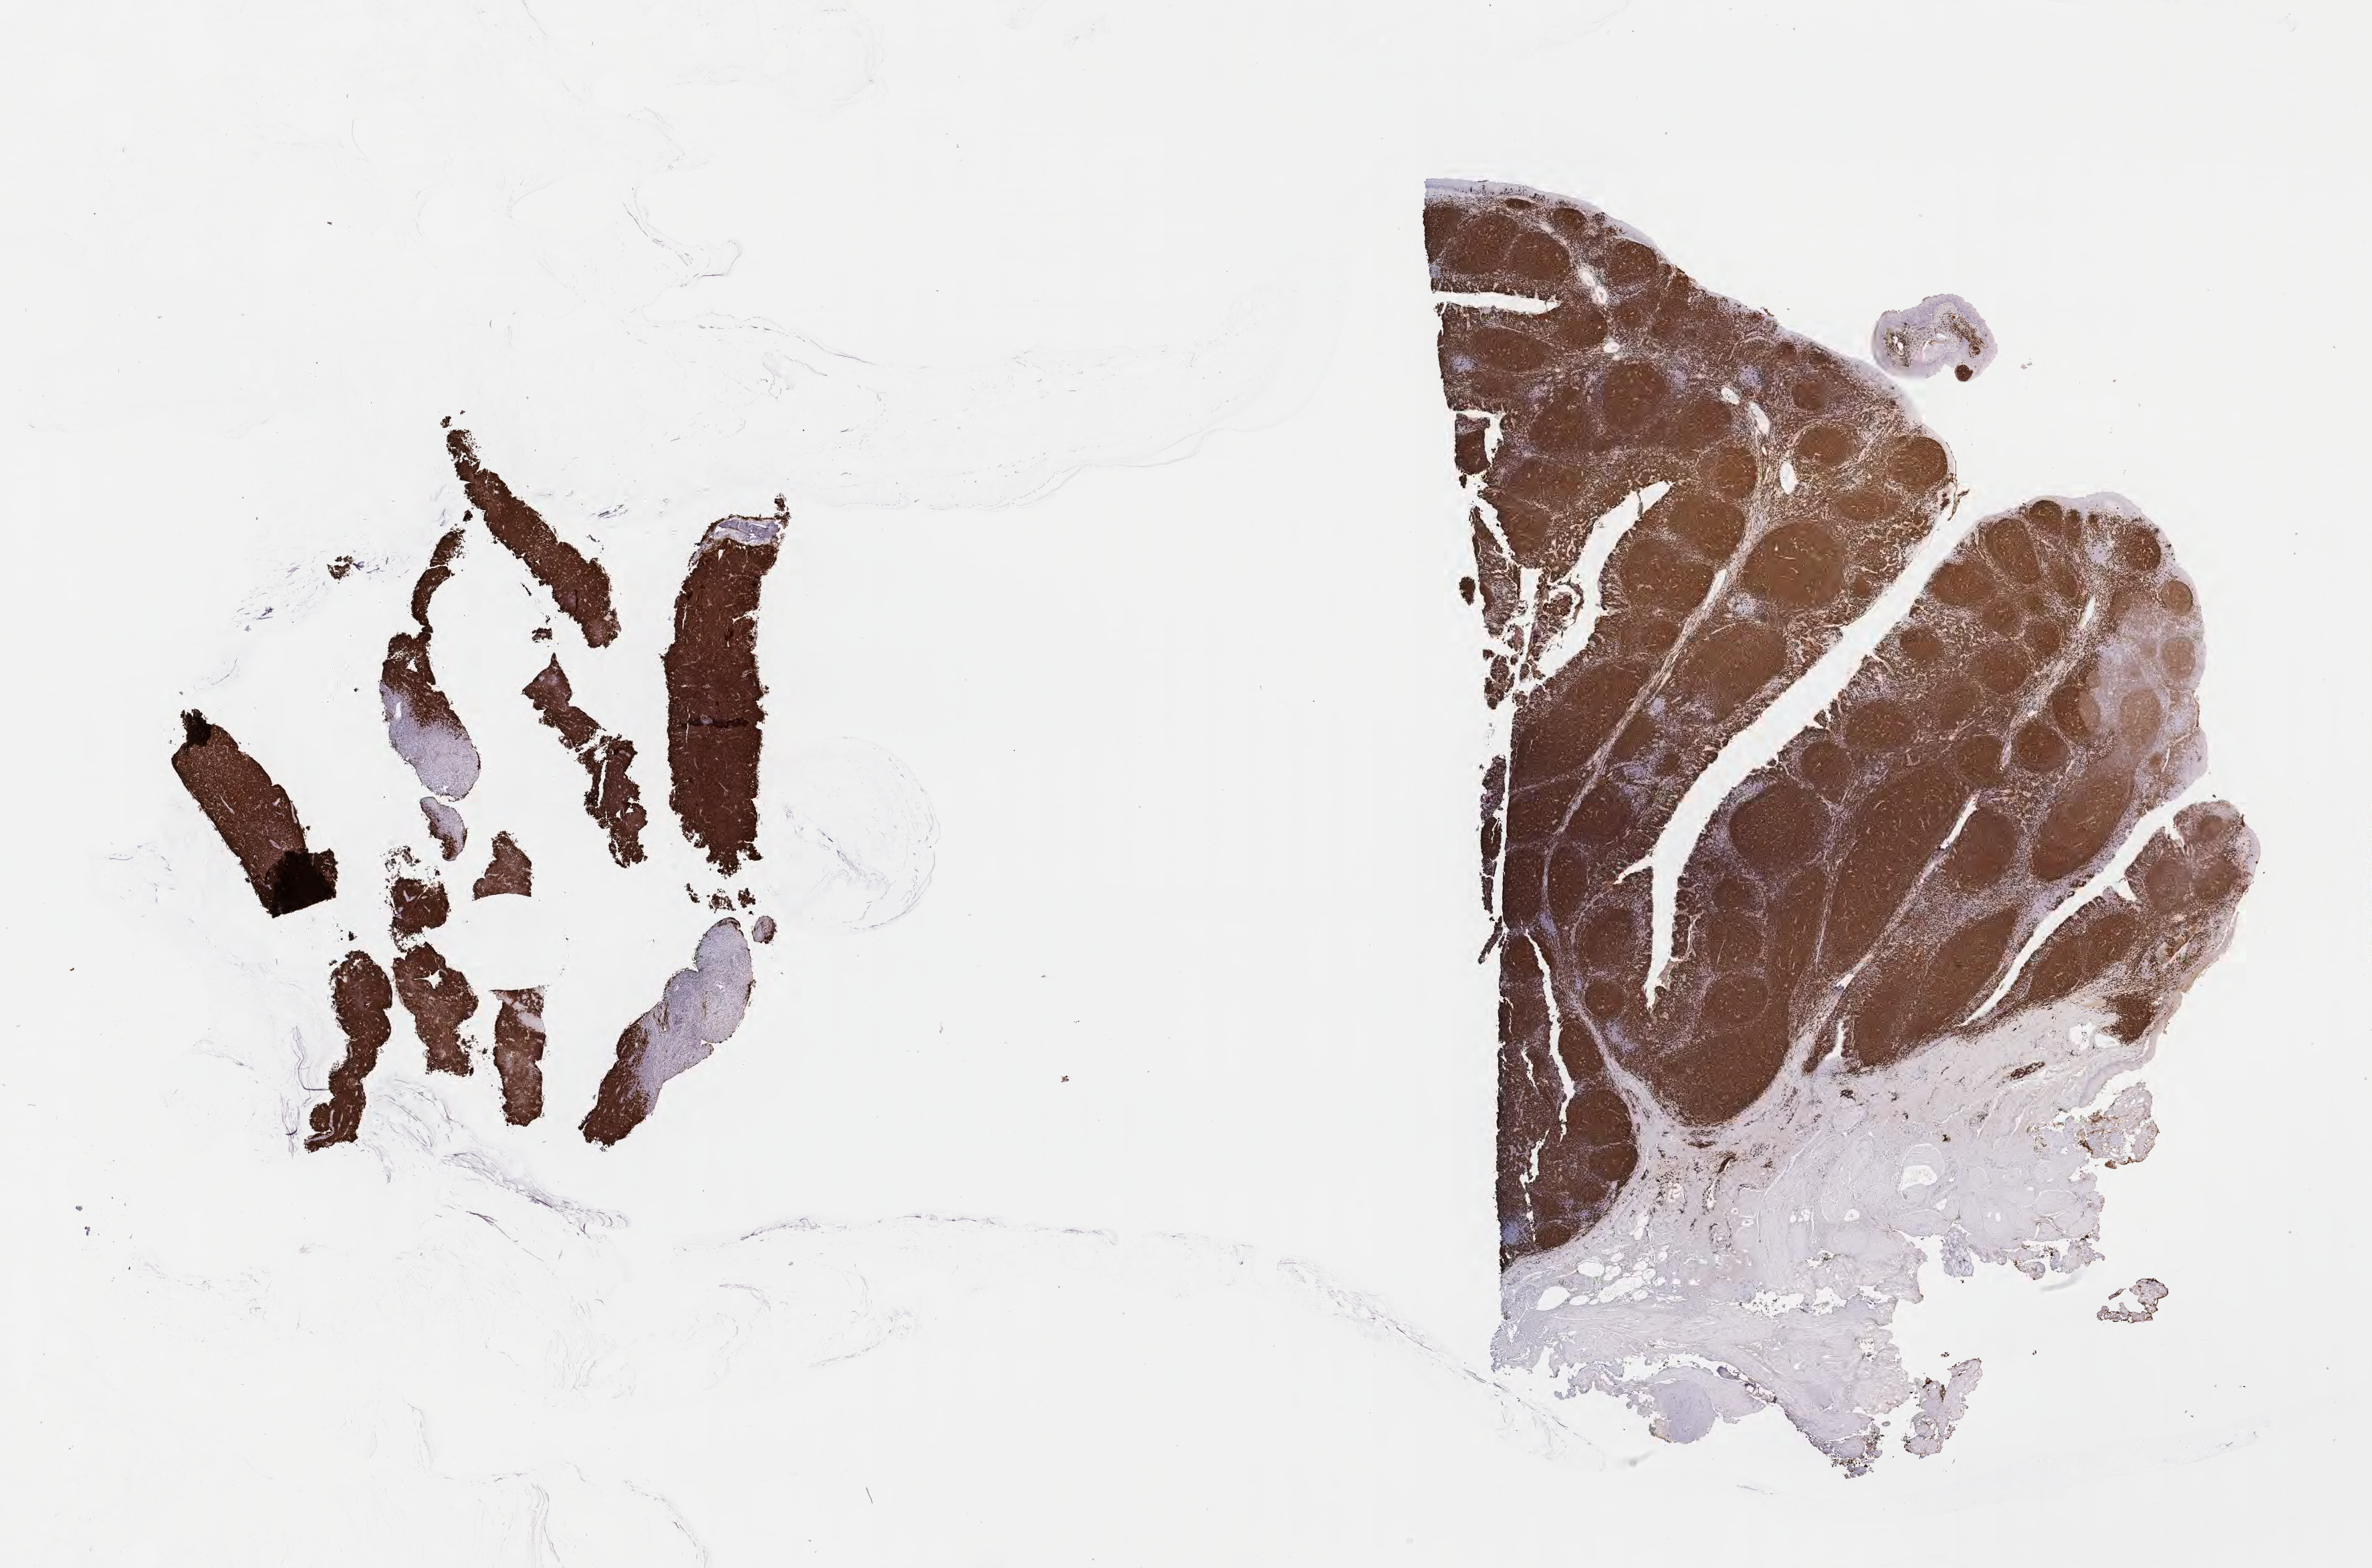
Whole-slide image, immunohistochemical stain for CD20, shown as a low-resolution overview of the whole scanned area (about 28.7 x 19.0 mm); specimen: tumor tissue; site: abdomen proper. Patient: male, age at initial diagnosis 7 years.
Histologic diagnosis: Burkitt lymphoma, NOS.